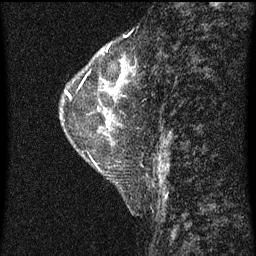
Breast MRI (dynamic contrast-enhanced), one sagittal slice. Slice 24 of 60 in the series (ordered by position). Dynamic contrast-enhanced series, image 2 of 4 at this slice position (ordered by acquisition). 1.5 T. TE 4.2 ms, TR 8 ms. 2 mm slice thickness. 256 × 256 image matrix. Patient: female, 56 years.
Structures marked on this image (semi-automatic segmentation, software-assisted and operator-edited):
- analysis volume of interest (the breast-tissue region the enhancement analysis was run in; not a lesion): bounding box [x1, y1, x2, y2] px = [62, 52, 135, 115]
- tumour enhancement mask (voxels above the 70 % enhancement threshold inside the analysis volume of interest): [106, 66, 125, 89]